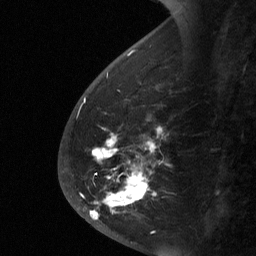
Breast MRI (dynamic contrast-enhanced), one sagittal slice; position 20 of 64 along the scan axis; dynamic contrast-enhanced study with each time point stored as its own series, time point 2 of 3 at this slice position (early post-contrast, ordered by acquisition time); 1.5 T; TE 4.8 ms, TR 27 ms; 2 mm slice thickness; 256 × 256 image matrix. Patient: female, 56 years. From the clinical record (not read from this slice): setting: breast cancer imaged before/during neoadjuvant chemotherapy; receptor status: HER2-positive.
Outlined on this slice (semi-automatically segmented with operator editing):
- analysis volume of interest (the breast-tissue region the enhancement analysis was run in; not a lesion): bounding box <59,110,170,229> (left, top, right, bottom; pixels)
- tumour enhancement mask (voxels above the 90 % enhancement threshold inside the analysis volume of interest): <89,127,163,220>